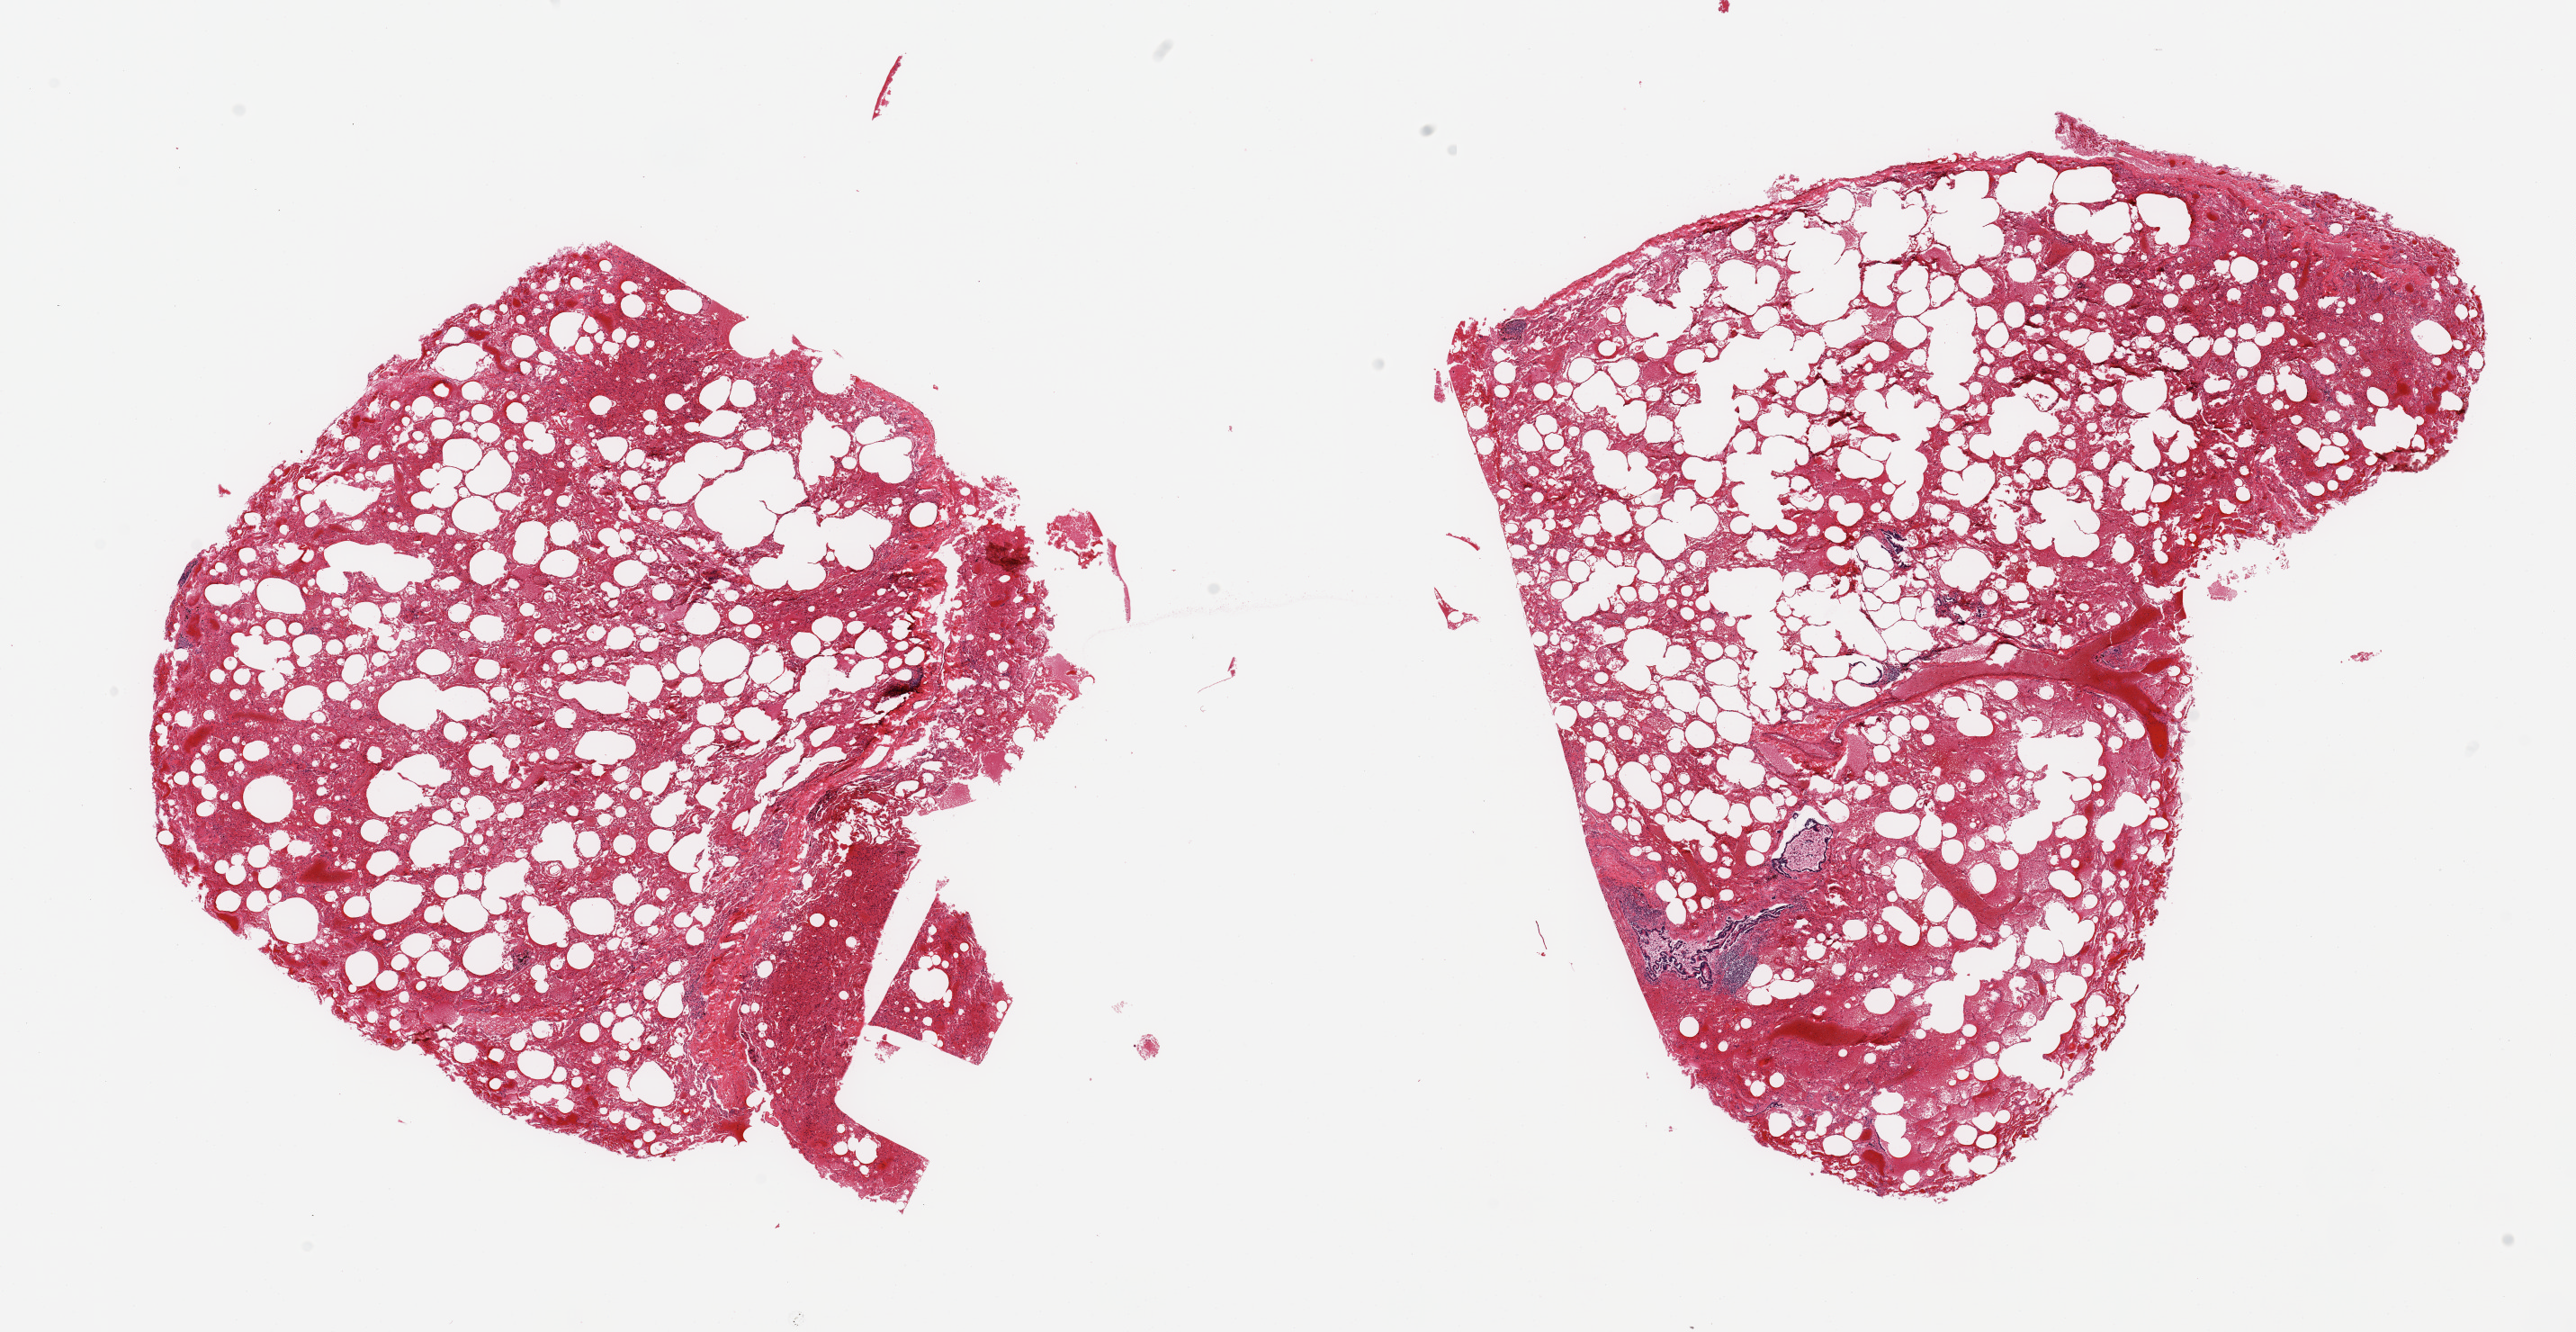
Digitized hematoxylin and eosin (H&E)-stained section, brightfield — a low-resolution overview of the entire scanned area, about 22.6 x 11.7 mm (acquisition: 20x scan). PAXgene-fixed, paraffin-embedded tissue. Sampled site (target tissue): lung. Donor tissue sample. Female donor.
* reviewer comment on this tissue sample: 2 pieces; alveolar hemorrhage